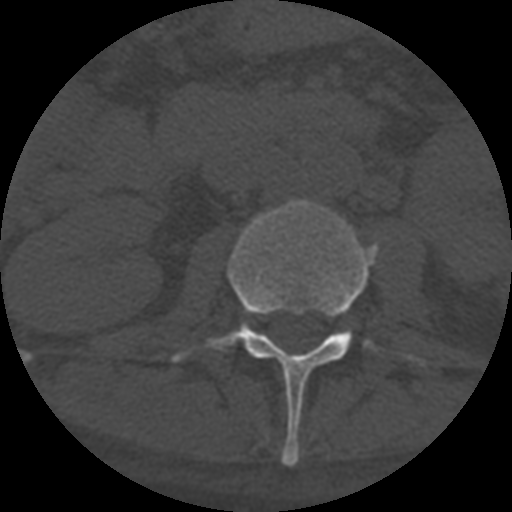
CT including the spine, one axial slice. Slice 258 of 708 in the series (ordered by position). Reconstruction kernel STANDARD. 120 kVp. One of 3 acquisitions stored at this slice position. Bone window (W 1800 / L 400 HU). 512 × 512 image matrix, field of view 160 × 160 mm. Patient age 55 years. Case-level facts recorded for this patient, not image findings: primary cancer: colon; vertebrae with lytic lesions (as recorded): T12, L1, L5.
Annotated regions visible in this slice (semi-automatic segmentation, software-assisted and operator-edited):
- L2 vertebra: bounding box [x1, y1, x2, y2] px = [172, 200, 423, 467]